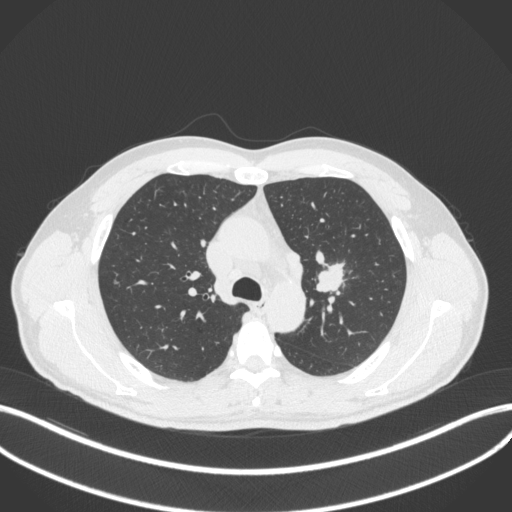
Chest CT, one axial slice; position 293 of 383 along the scan axis; reconstruction kernel B31f; lung window (W 1500 / L -600 HU); 1 mm slice thickness; 512 × 512 image matrix, field of view 400 × 400 mm. Patient: male, 50 years. From the clinical record (not read from this slice): clinical TNM (as recorded): T1c N1 M1b.
Structures marked on this image (bounding box drawn by a radiologist):
- lung tumour (recorded histology: squamous cell carcinoma): bounding box (x1, y1, x2, y2) in pixels: (310, 255, 347, 295)